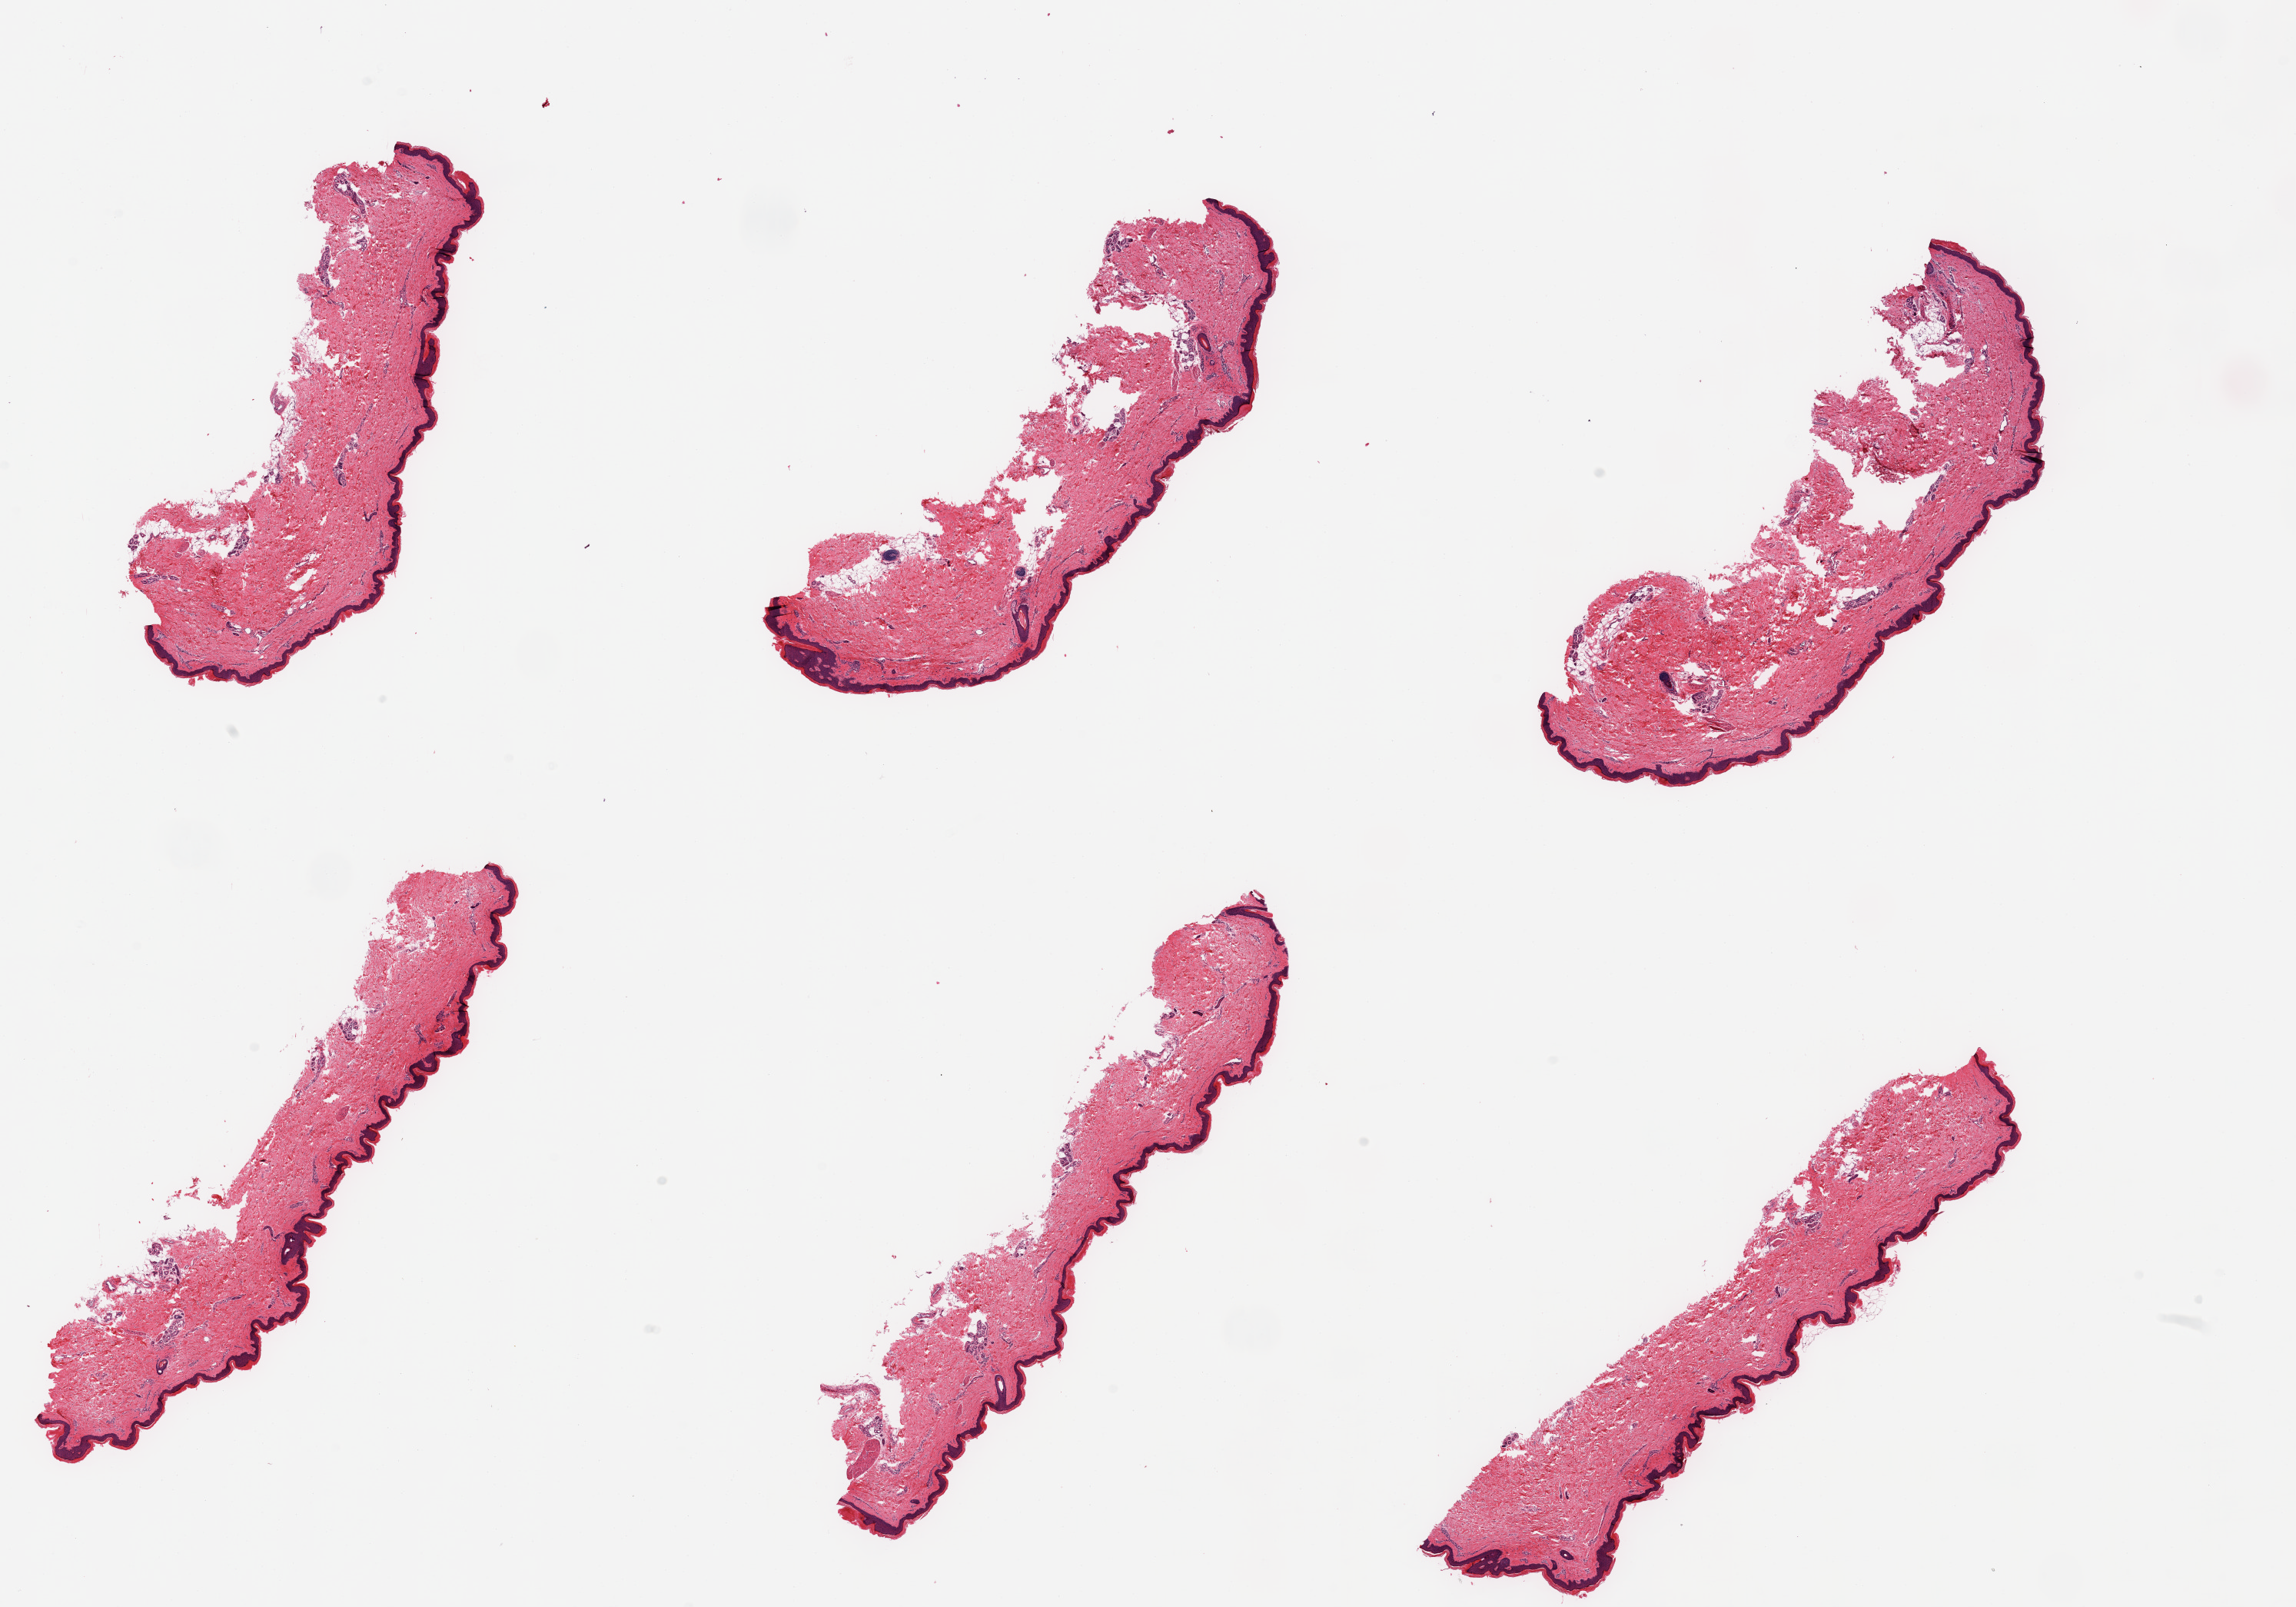
Hematoxylin and eosin (H&E) whole-slide image, whole scanned area (about 23.6 x 16.5 mm) shown as a low-resolution overview. PAXgene-fixed paraffin-embedded (PFPE) section. Sampled site (target tissue): skin of lower leg. Tissue donor sample. Donor sex: female.
• pathologist's review note for this sample: 6 pieces; minimal dermal fat content